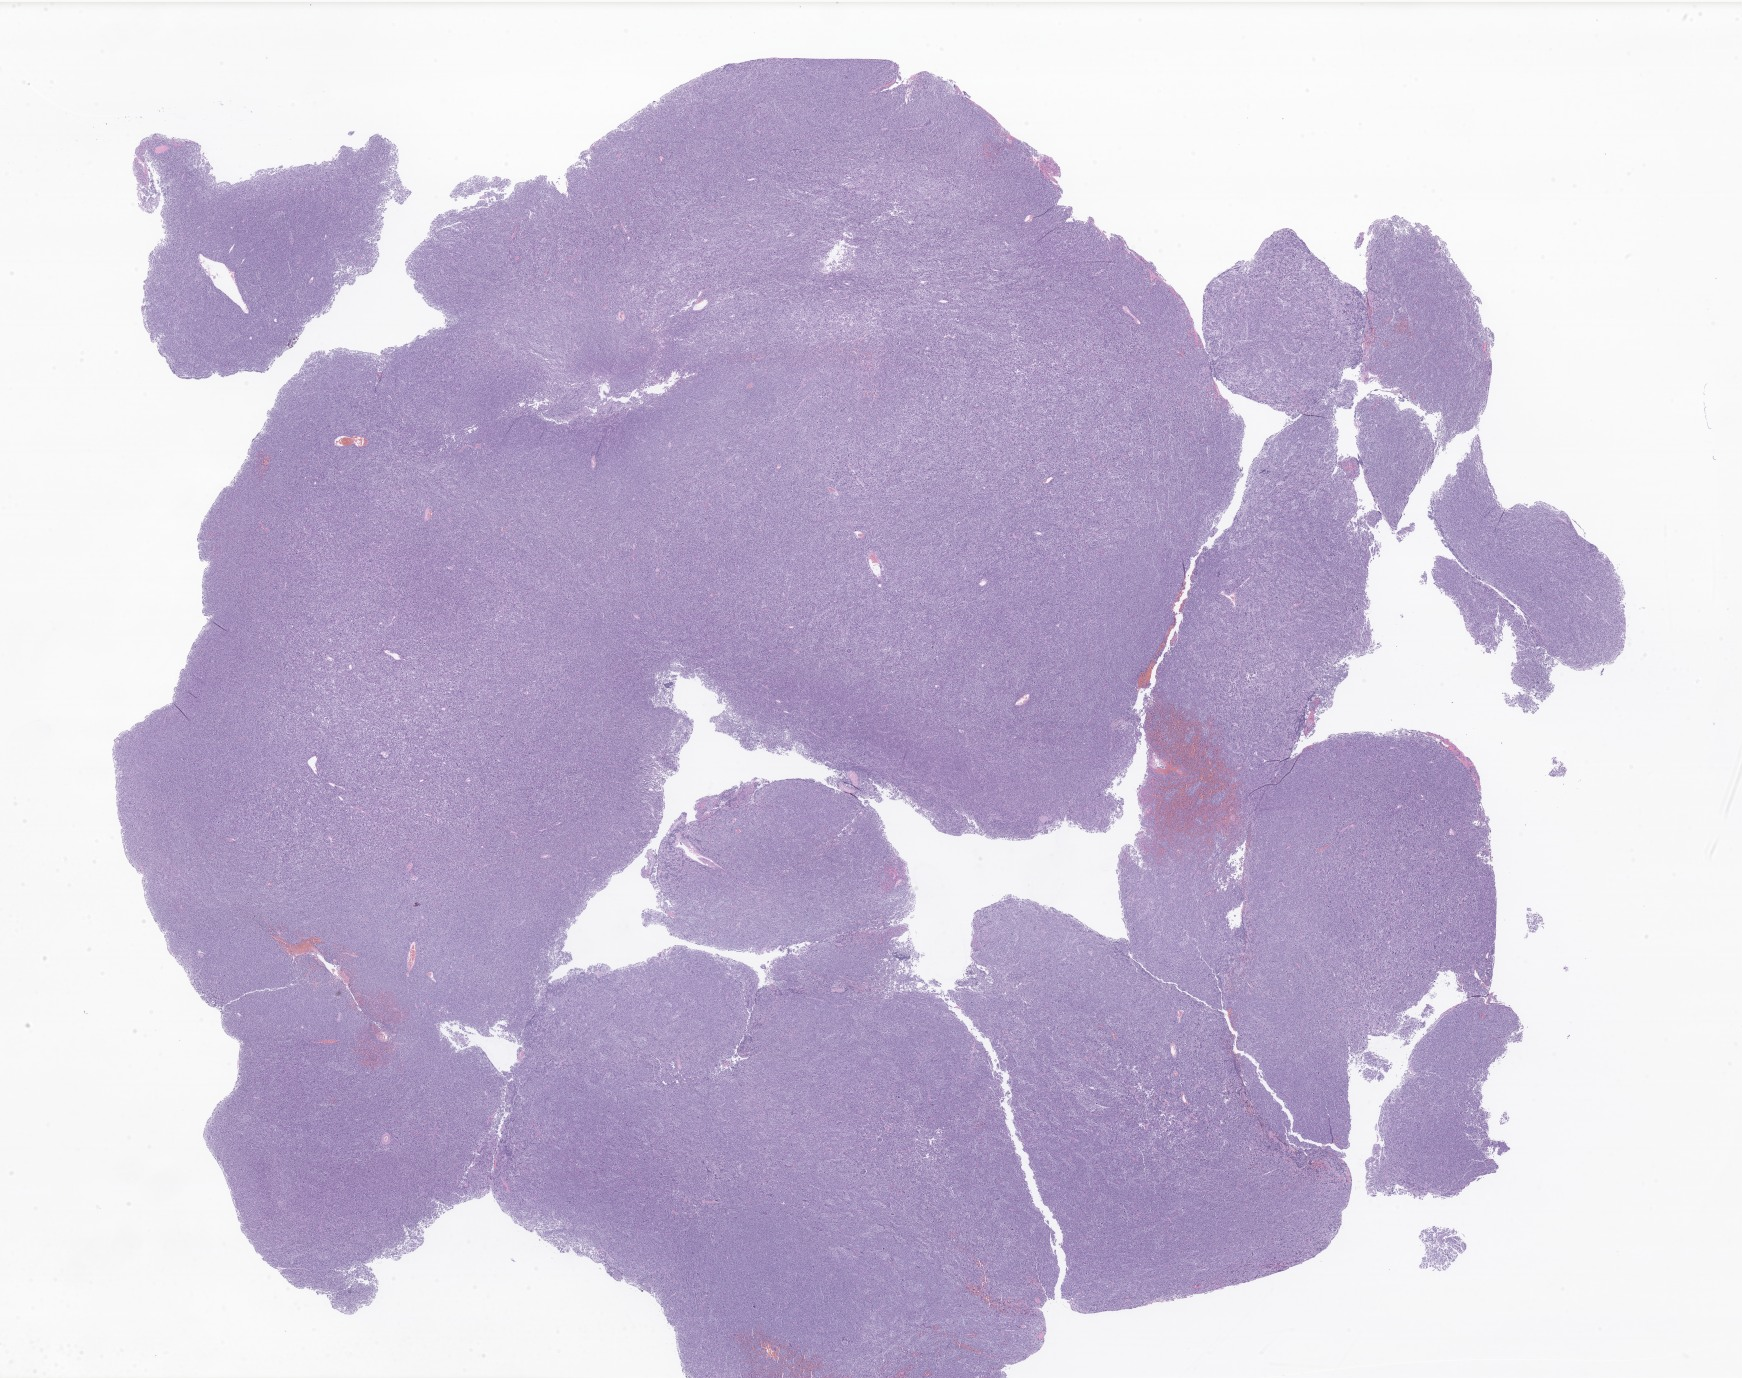
Digitized H&E-stained section of tumor tissue from the brain — low-resolution overview of the scanned area, about 29.4 x 23.2 mm; formalin-fixed paraffin-embedded section. Patient female; age 190 months (15 years 10 months).
Diagnosis (ICD-O-3 morphology term): Medulloblastoma, NOS.